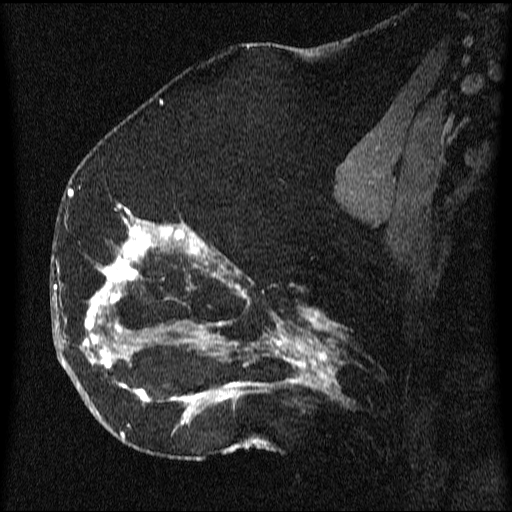
Breast MRI (dynamic contrast-enhanced), one sagittal slice; position 32 of 64 along the scan axis; dynamic contrast-enhanced series, image 2 of 3 at this slice position (ordered by acquisition); 1.5 T; TE 4.2 ms, TR 9.1 ms; 2.2 mm slice thickness; 512 × 512 image matrix, field of view 180 × 180 mm. Female patient, age 52 years.
Outlined on this slice (semi-automatic segmentation, software-assisted and operator-edited):
- analysis volume of interest (the breast-tissue region the enhancement analysis was run in; not a lesion): bounding box [x1, y1, x2, y2] px = [61, 203, 350, 438]
- tumour enhancement mask (voxels above the 70 % enhancement threshold inside the analysis volume of interest): [65, 205, 339, 438]